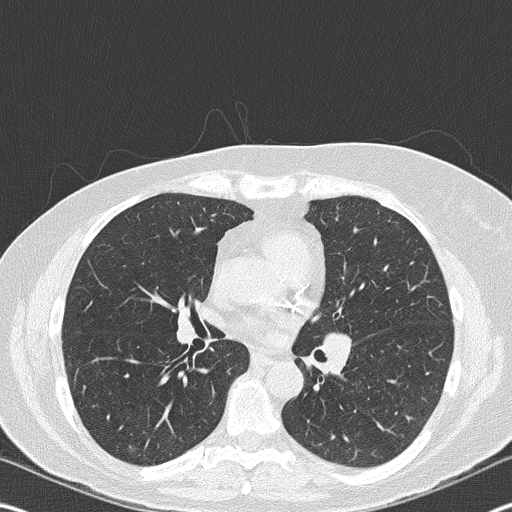
Low-dose screening chest CT, one axial slice; slice 95 of 177 in the series (ordered by position); lung window (W 1500 / L -600 HU); 2 mm slice thickness; 512 × 512 image matrix, field of view 342 × 342 mm.
Outlined on this slice (expert manual segmentation):
- lesion 2 (nodule, hilum of left lung): bounding box [x1, y1, x2, y2] px = [326, 333, 352, 370]